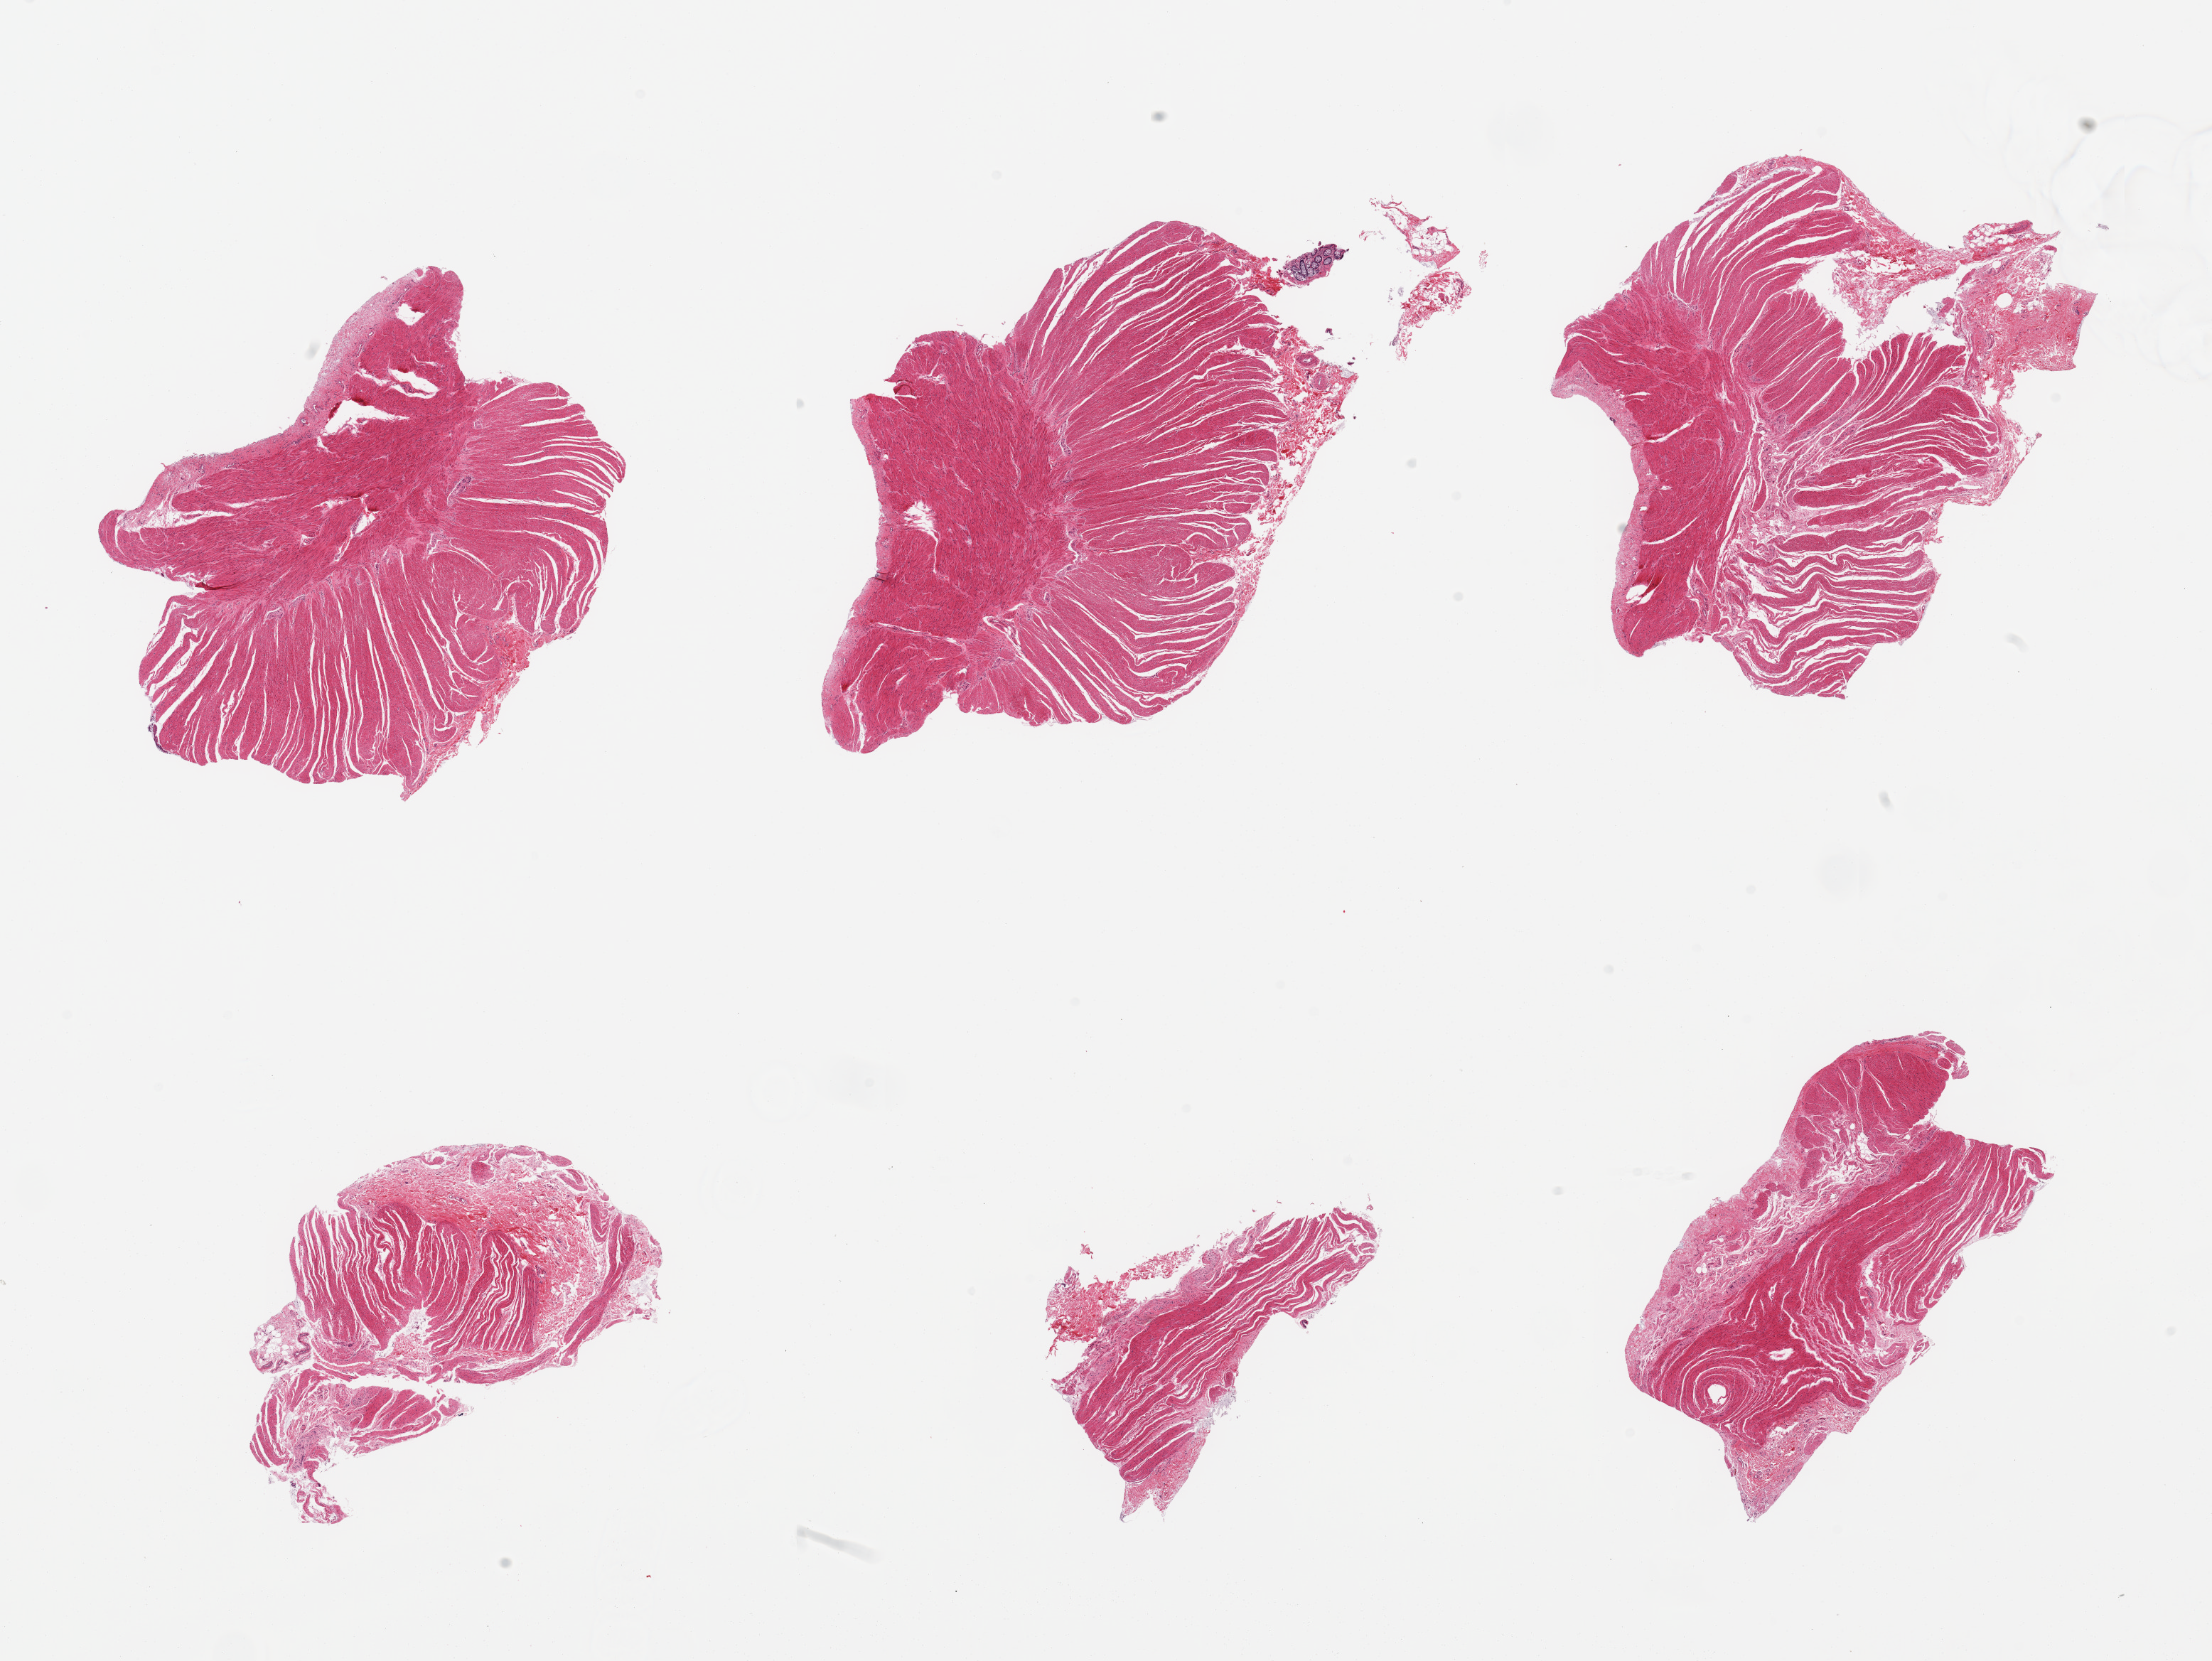
Digitized haematoxylin and eosin-stained section, whole scanned area (about 24.6 x 18.5 mm, acquisition: 20x scan) shown as a low-resolution overview. PAXgene-fixed, paraffin-embedded tissue. Section of sigmoid colon (target tissue). Tissue donor sample. Donor sex: female.
Pathologist's review note for this sample: 6 pieces, all muscularis, good specimens.